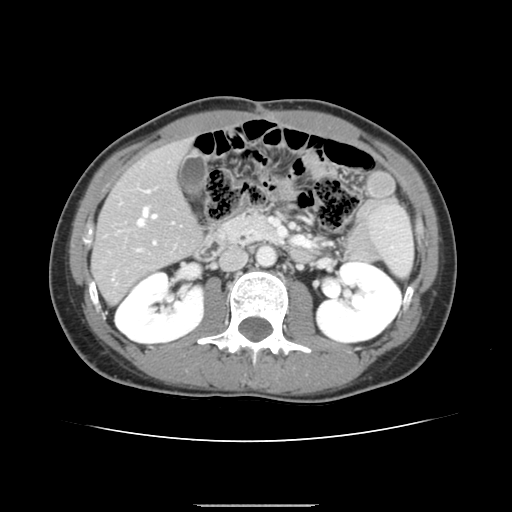
Contrast-enhanced abdominal CT, one axial slice; position 66 of 150 along the scan axis; intravenous contrast given; soft-tissue window (W 400 / L 40 HU); 512 × 512 image matrix, field of view 324 × 324 mm. Female patient, age 32 years. From the clinical record (not read from this slice): diagnosis: colorectal cancer liver metastases, imaged before liver resection; multiple liver metastases: yes; largest metastasis: 0.7 cm; disease in both lobes: no.
Annotated regions visible in this slice (outlined manually by an expert reader):
- hepatic veins: bounding box [x1, y1, x2, y2] px = [138, 207, 156, 225]
- liver: [93, 143, 200, 301]
- planned liver remnant (the part of the liver to remain after resection): [94, 142, 200, 291]
- portal vein (with intrahepatic branches): [137, 190, 156, 251]